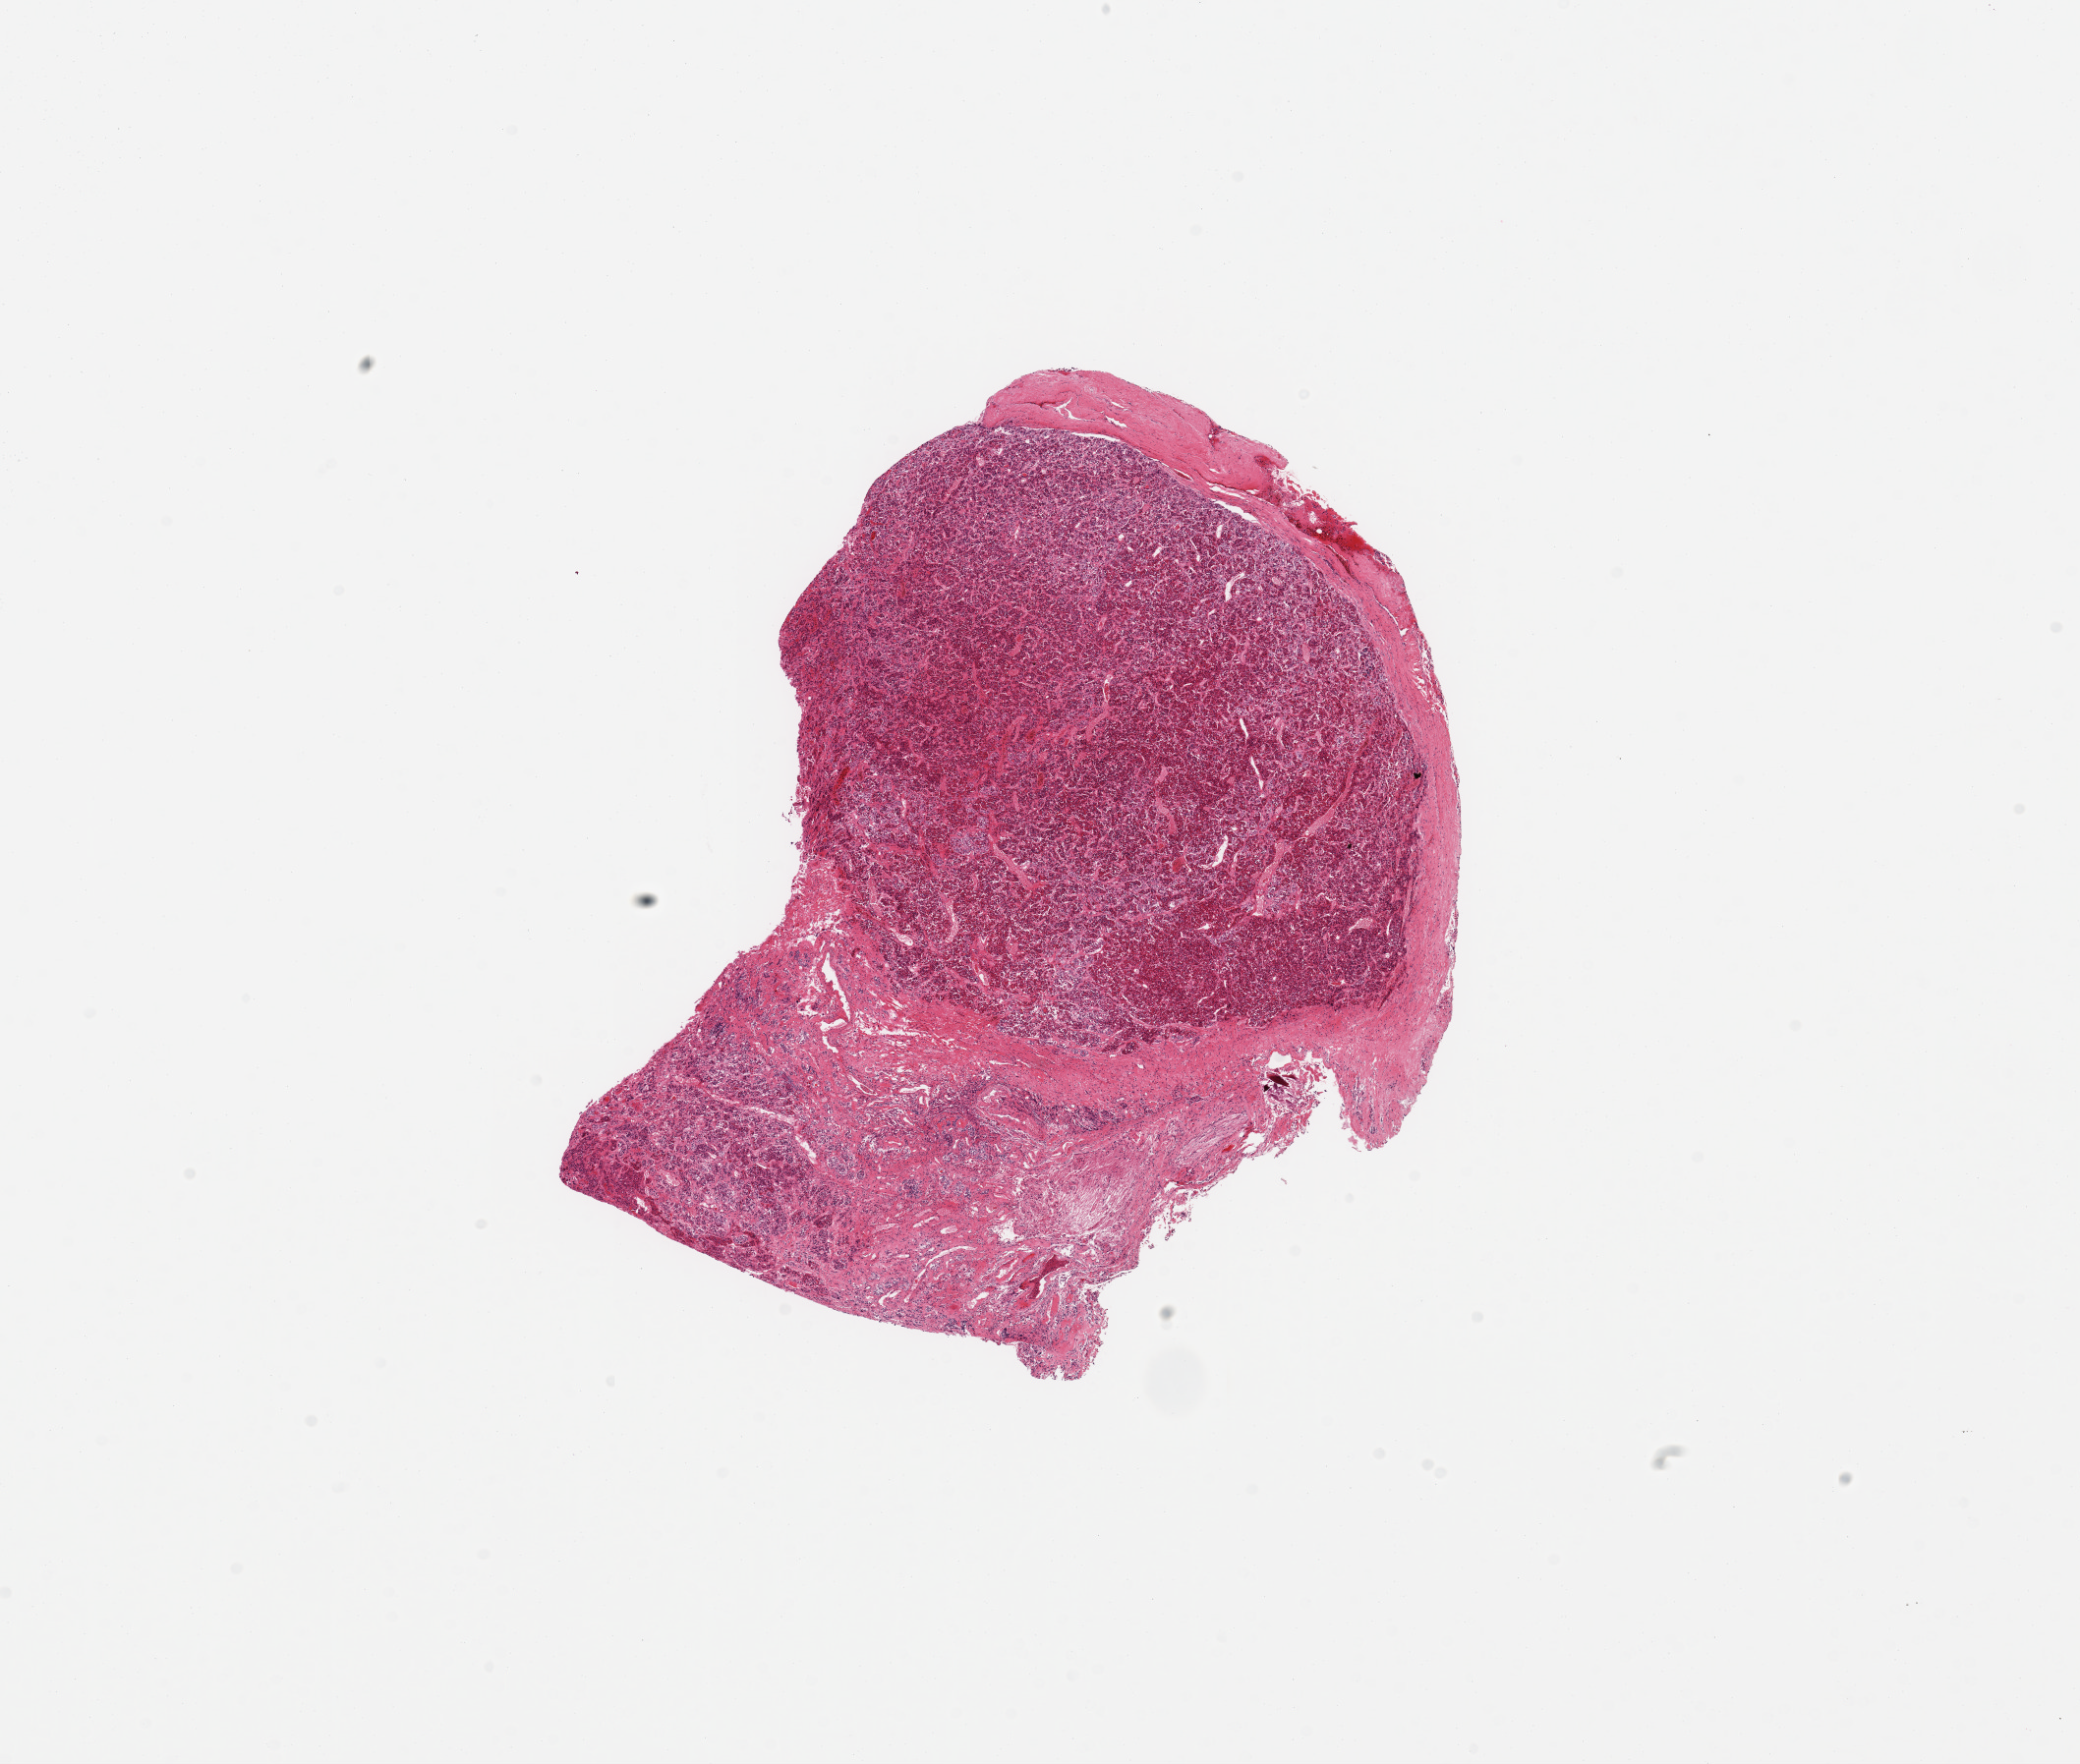
Whole-slide image, haematoxylin and eosin stain, brightfield, low-resolution overview of the scanned area, about 16.7 x 14.2 mm. PAXgene-fixed, paraffin-embedded tissue. Section of pituitary (target tissue). Donor tissue sample. Donor sex: male.
* reviewer comment on this tissue sample: 1 piece, mainly adenohypophysis and dura; ~3x2mm nubbin of neurohypophysis